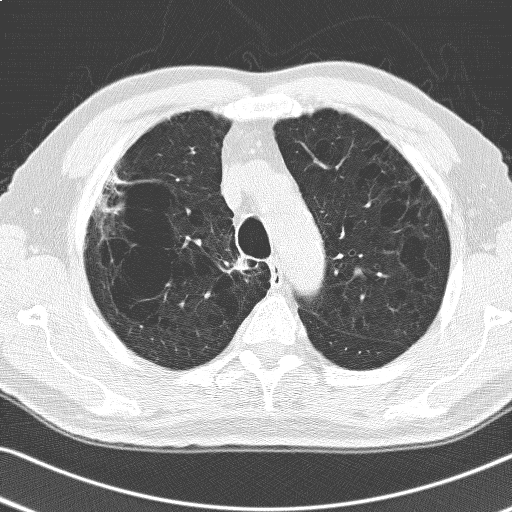
Low-dose screening chest CT, one axial slice. Slice 133 of 168 in the series (ordered by position). 120 kVp. Lung window (W 1500 / L -600 HU). 3.2 mm slice thickness. 512 × 512 image matrix, field of view 336 × 336 mm.
Structures marked on this image (expert manual segmentation):
- lesion 1 (tumor, upper lobe of right lung): bounding box (x1, y1, x2, y2) in pixels: (105, 171, 127, 190)